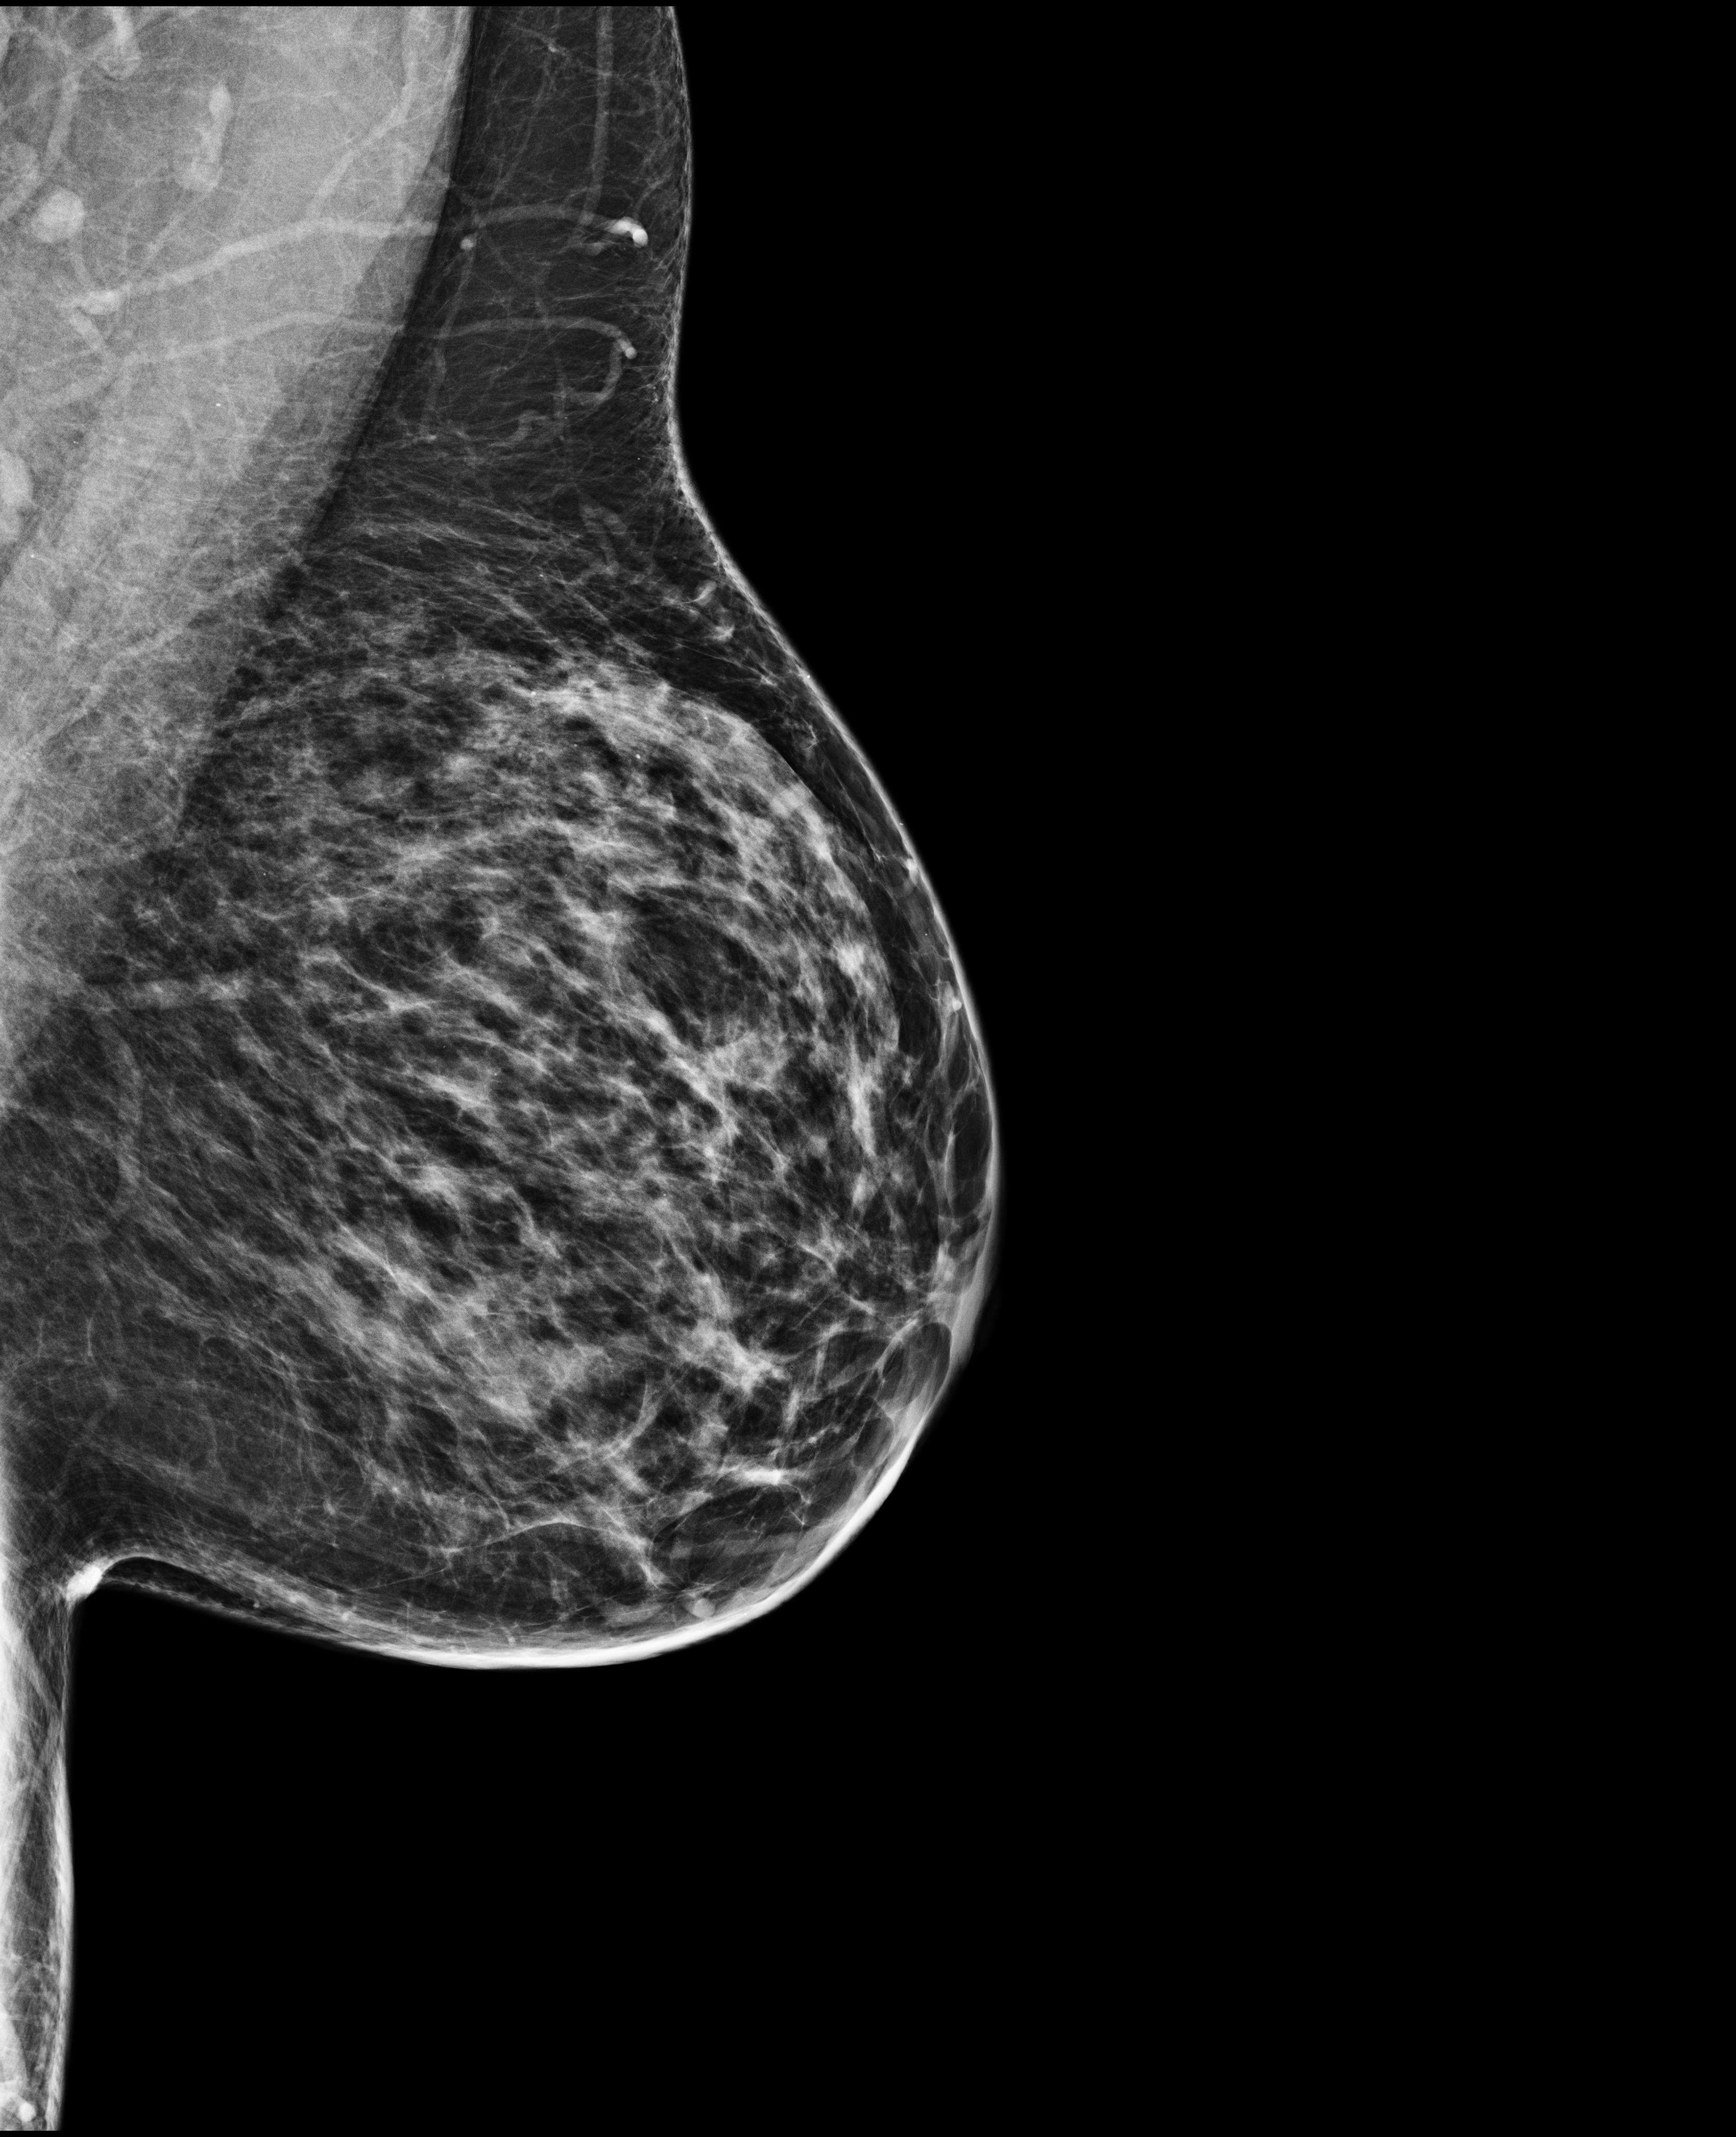
Digital mammogram (FFDM), left breast, medio-lateral oblique projection, screening examination, compressed breast thickness 71 mm, system: Selenia Dimensions. Female patient, age 47 years.
Breast density at the screening exam (both breasts): heterogeneously dense (BI-RADS density category c). Final BI-RADS assessment for this screening round (tomosynthesis exam, both breasts): category 1. Recall: no recall after this screen.